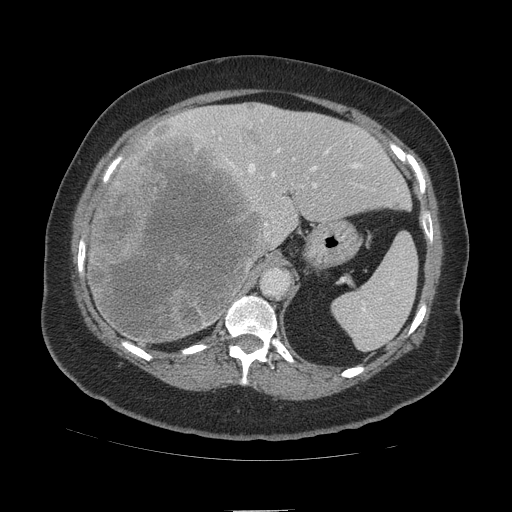
Contrast-enhanced abdominal CT (liver protocol), one axial slice; position 73 of 109 along the scan axis; 140 kVp; soft-tissue window (W 400 / L 40 HU); 2.5 mm slice thickness; 512 × 512 image matrix. From the clinical record (not read from this slice): diagnosis: hepatocellular carcinoma (patient treated with transarterial chemoembolisation; whether this scan precedes or follows treatment is not stated here); TNM stage (as recorded): Stage-IVB; Child-Pugh class: A; tumour nodularity: multinodular.
Annotated regions visible in this slice (semi-automatic segmentation, software-assisted and operator-edited):
- liver parenchyma outside the tumour (the mass and vessels are separate outlines, so this box may not span the whole liver): box from (x=88, y=104) to (x=410, y=340) px
- mass: (x=88, y=122)–(x=272, y=349)
- liver vessels: (x=188, y=114)–(x=398, y=190)